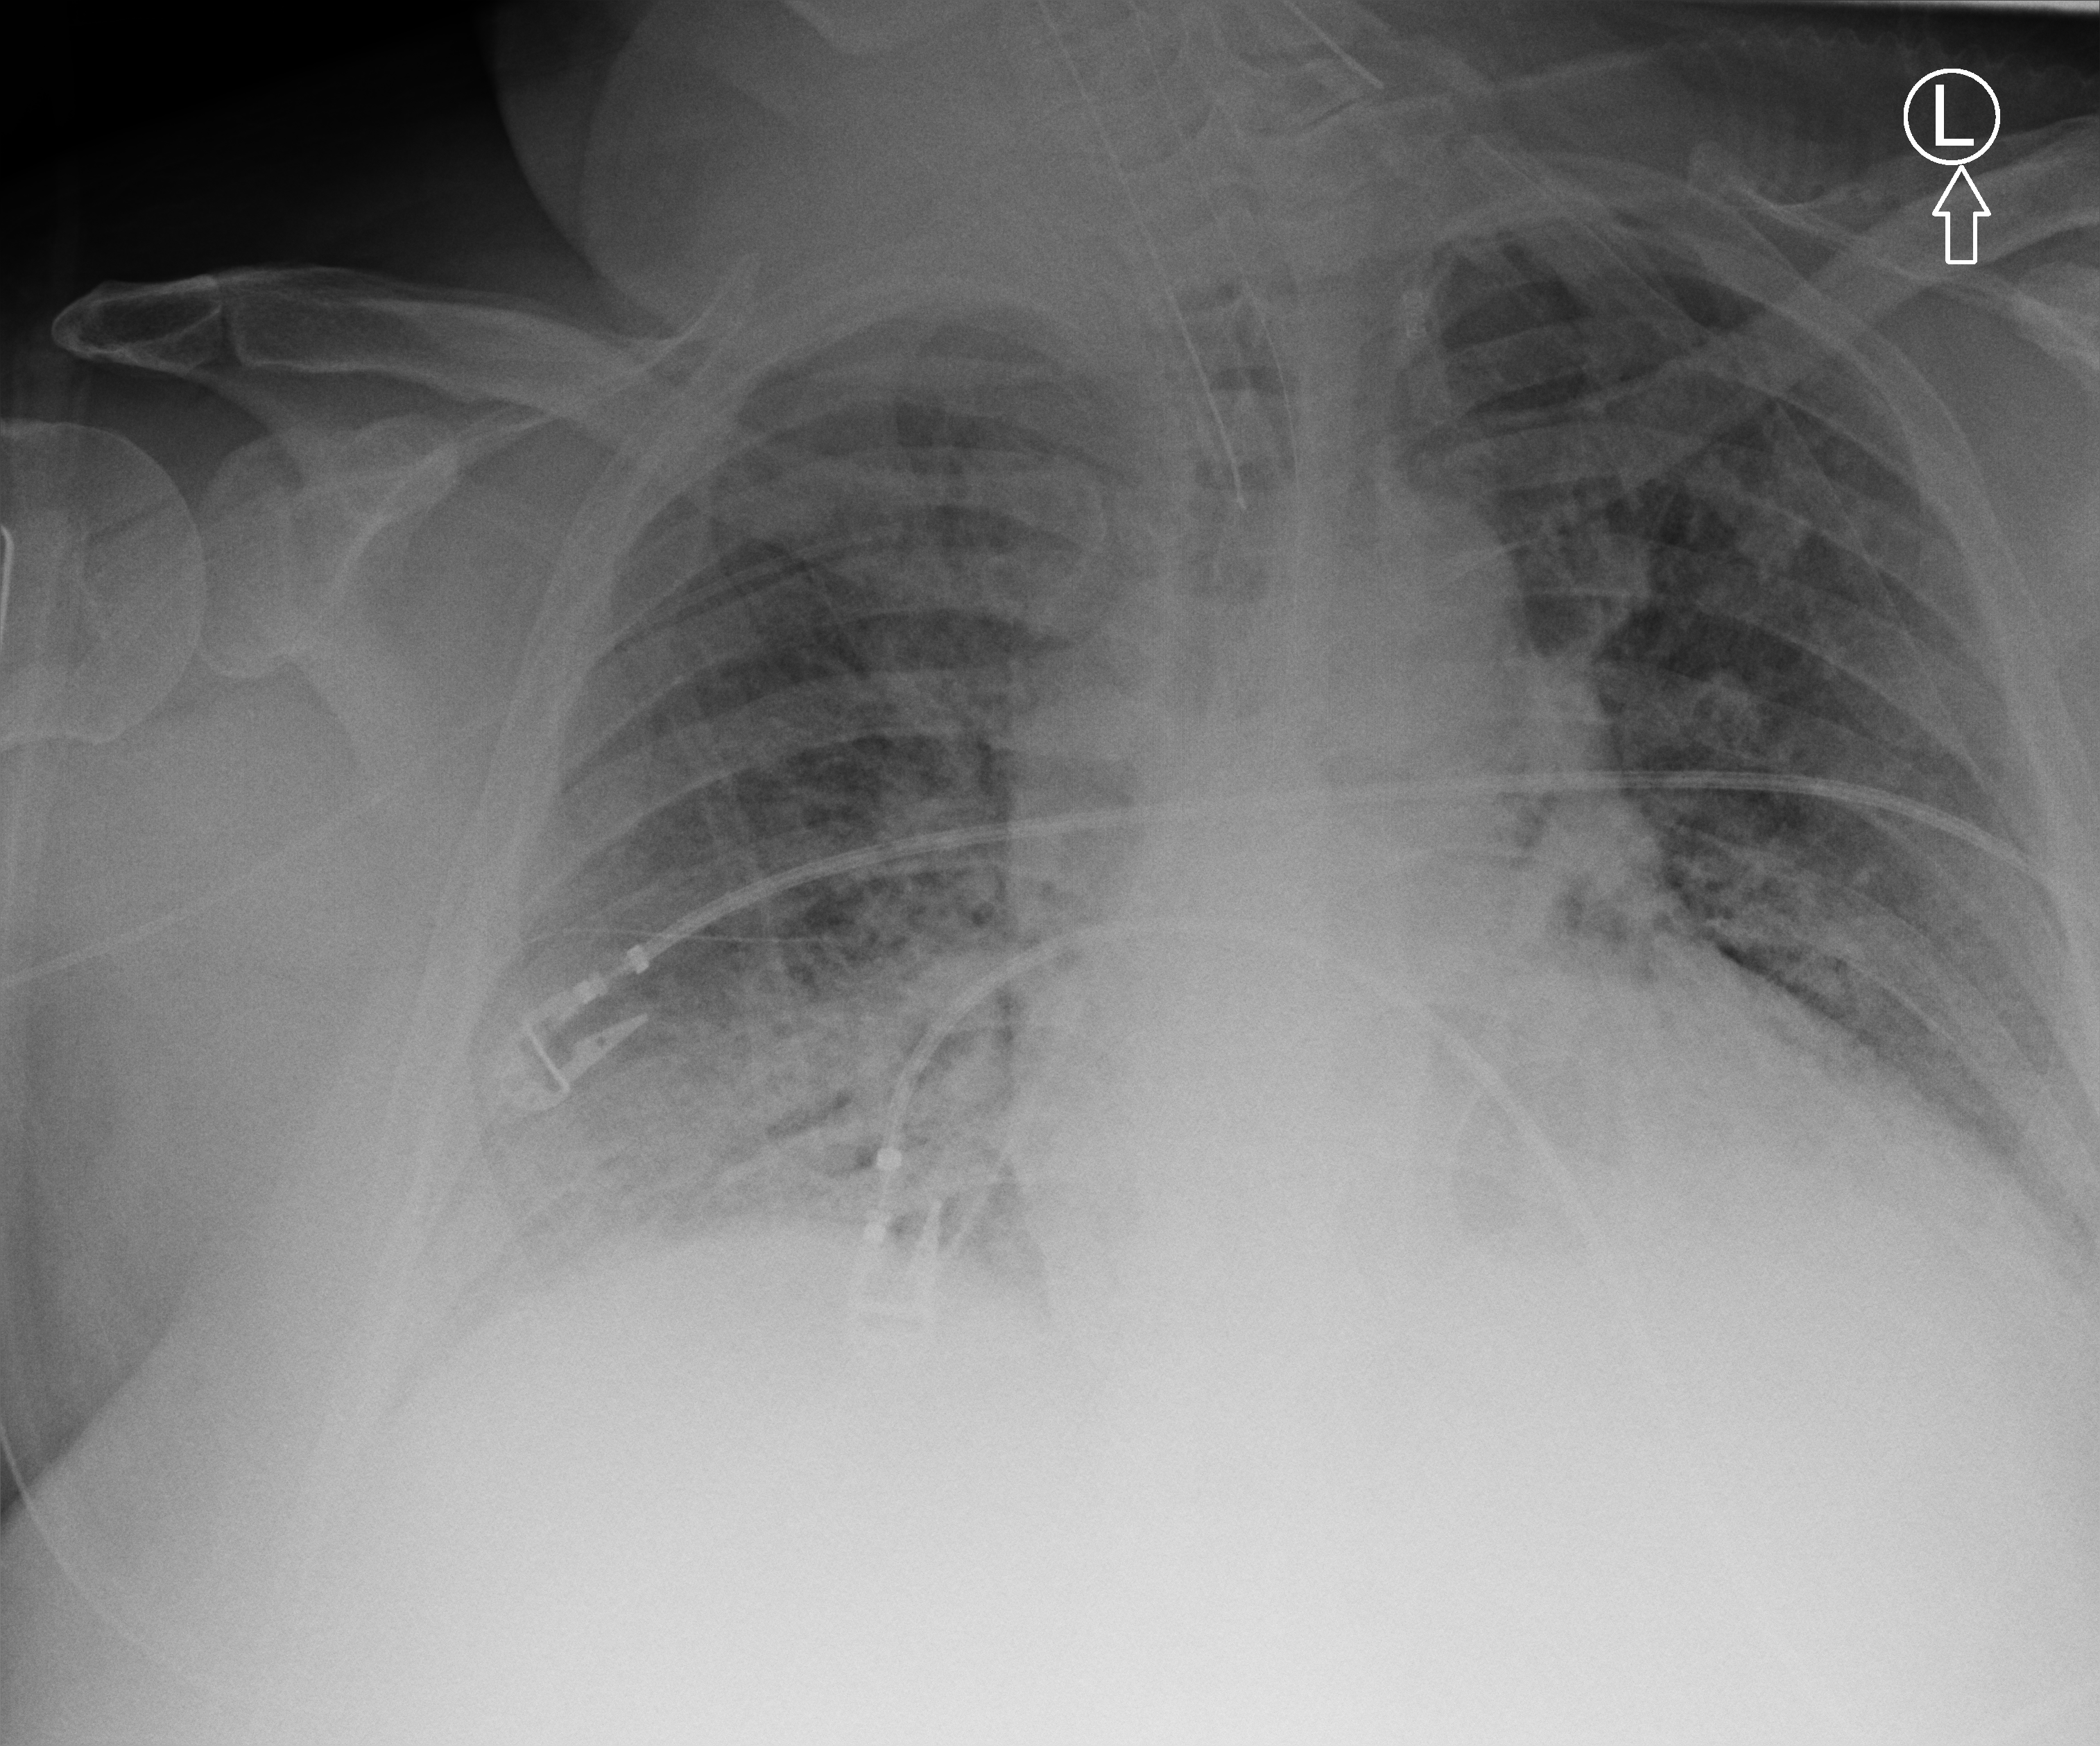
Chest X-ray (portable), anteroposterior (AP) projection. Adult patient hospitalised with COVID-19, age 18–59 years.
Admission-level facts for this patient (not findings on this image; timing relative to this image not recorded): length of hospital stay: 26 days; smoking status (admission record): never; mechanically ventilated during this hospital stay: yes.